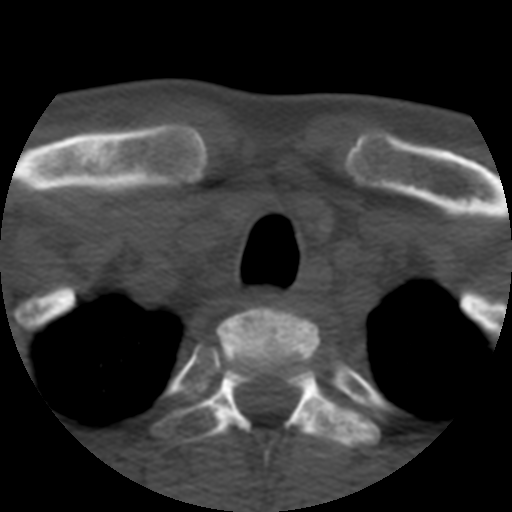
CT including the spine, one axial slice; slice 437 of 508 in the series (ordered by position); reconstruction kernel STANDARD; bone window (W 1800 / L 400 HU); 1.25 mm slice thickness; 512 × 512 image matrix, field of view 160 × 160 mm. Patient age 57 years. From the clinical record (not read from this slice): primary cancer: prostate.
Outlined on this slice (semi-automatic segmentation, software-assisted and operator-edited):
- T1 vertebra: box from (x=217, y=306) to (x=320, y=360) px
- T2 vertebra: (x=150, y=350)–(x=380, y=461)